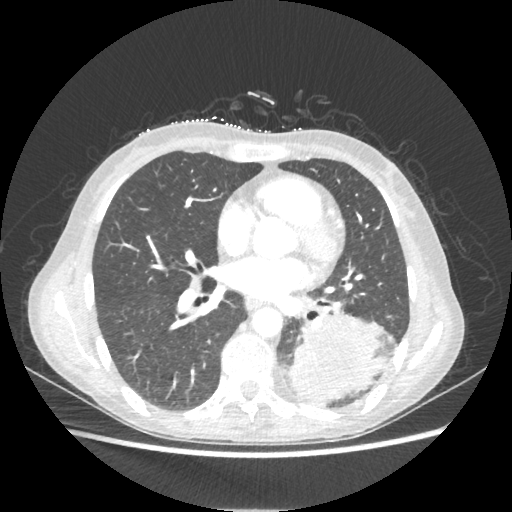
Chest CT, one axial slice. Reconstruction kernel STANDARD. 80 kVp. Lung window (W 1500 / L -600 HU). 1.25 mm slice thickness. 512 × 512 image matrix, field of view 360 × 360 mm. Female patient, age 53 years. From the clinical record (not read from this slice): clinical TNM (as recorded): T3 N0 M0.
Outlined on this slice (bounding box drawn by a radiologist):
- lung tumour (recorded histology: adenocarcinoma): box from (x=287, y=317) to (x=386, y=407) px